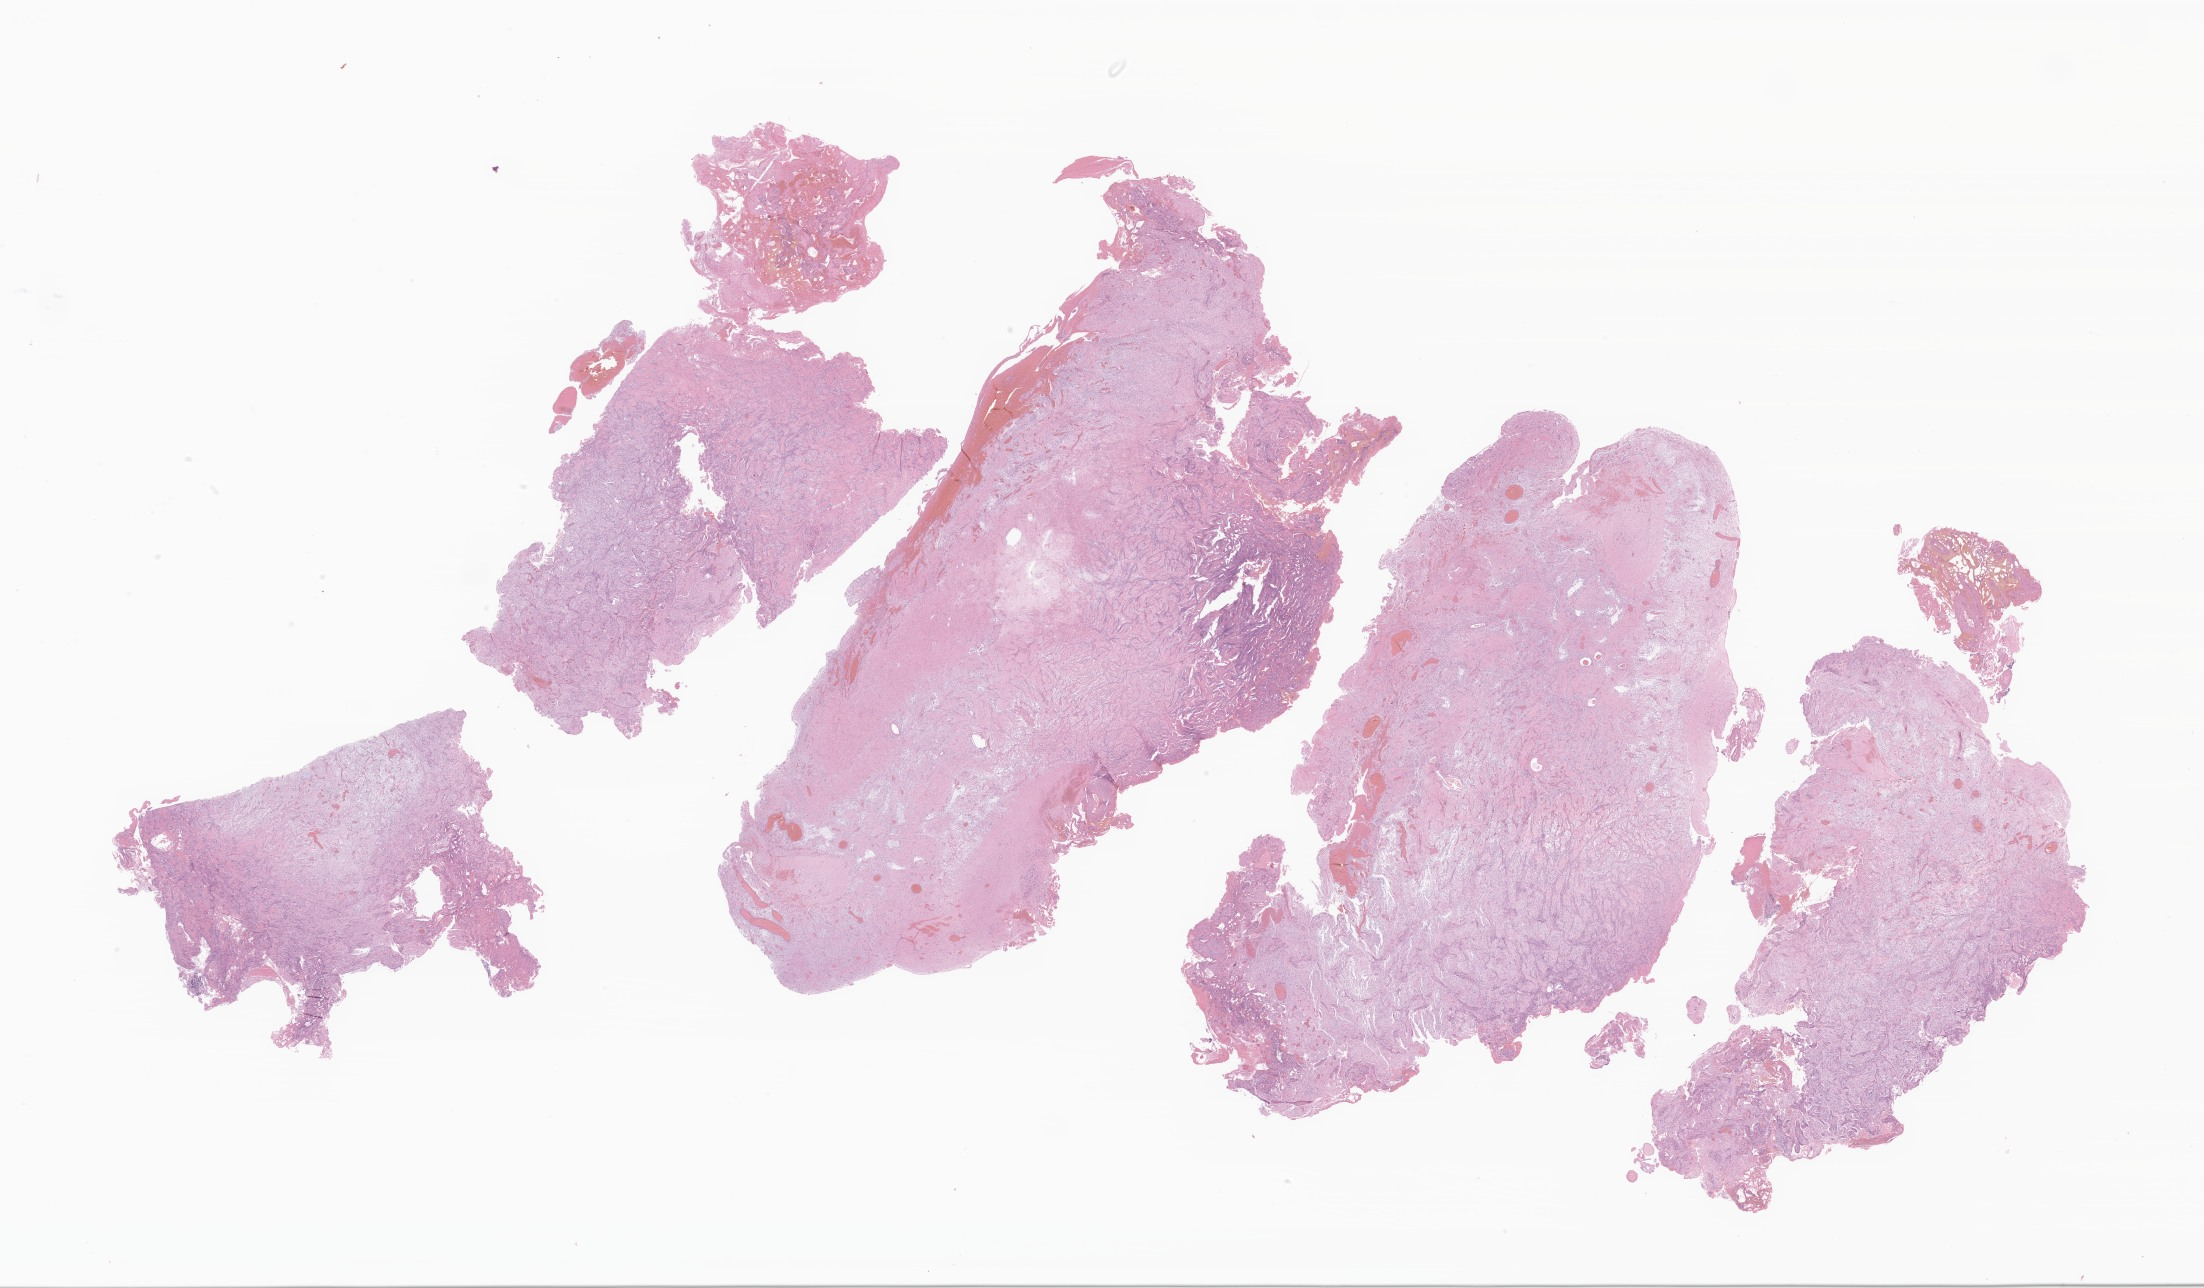
H&E whole-slide image of tumor tissue from the brain — a low-resolution overview of the entire scanned area, about 37.2 x 21.7 mm; formalin-fixed paraffin-embedded section. Patient male; age 51 months (4 years 3 months).
Recorded diagnosis: Pilocytic astrocytoma.